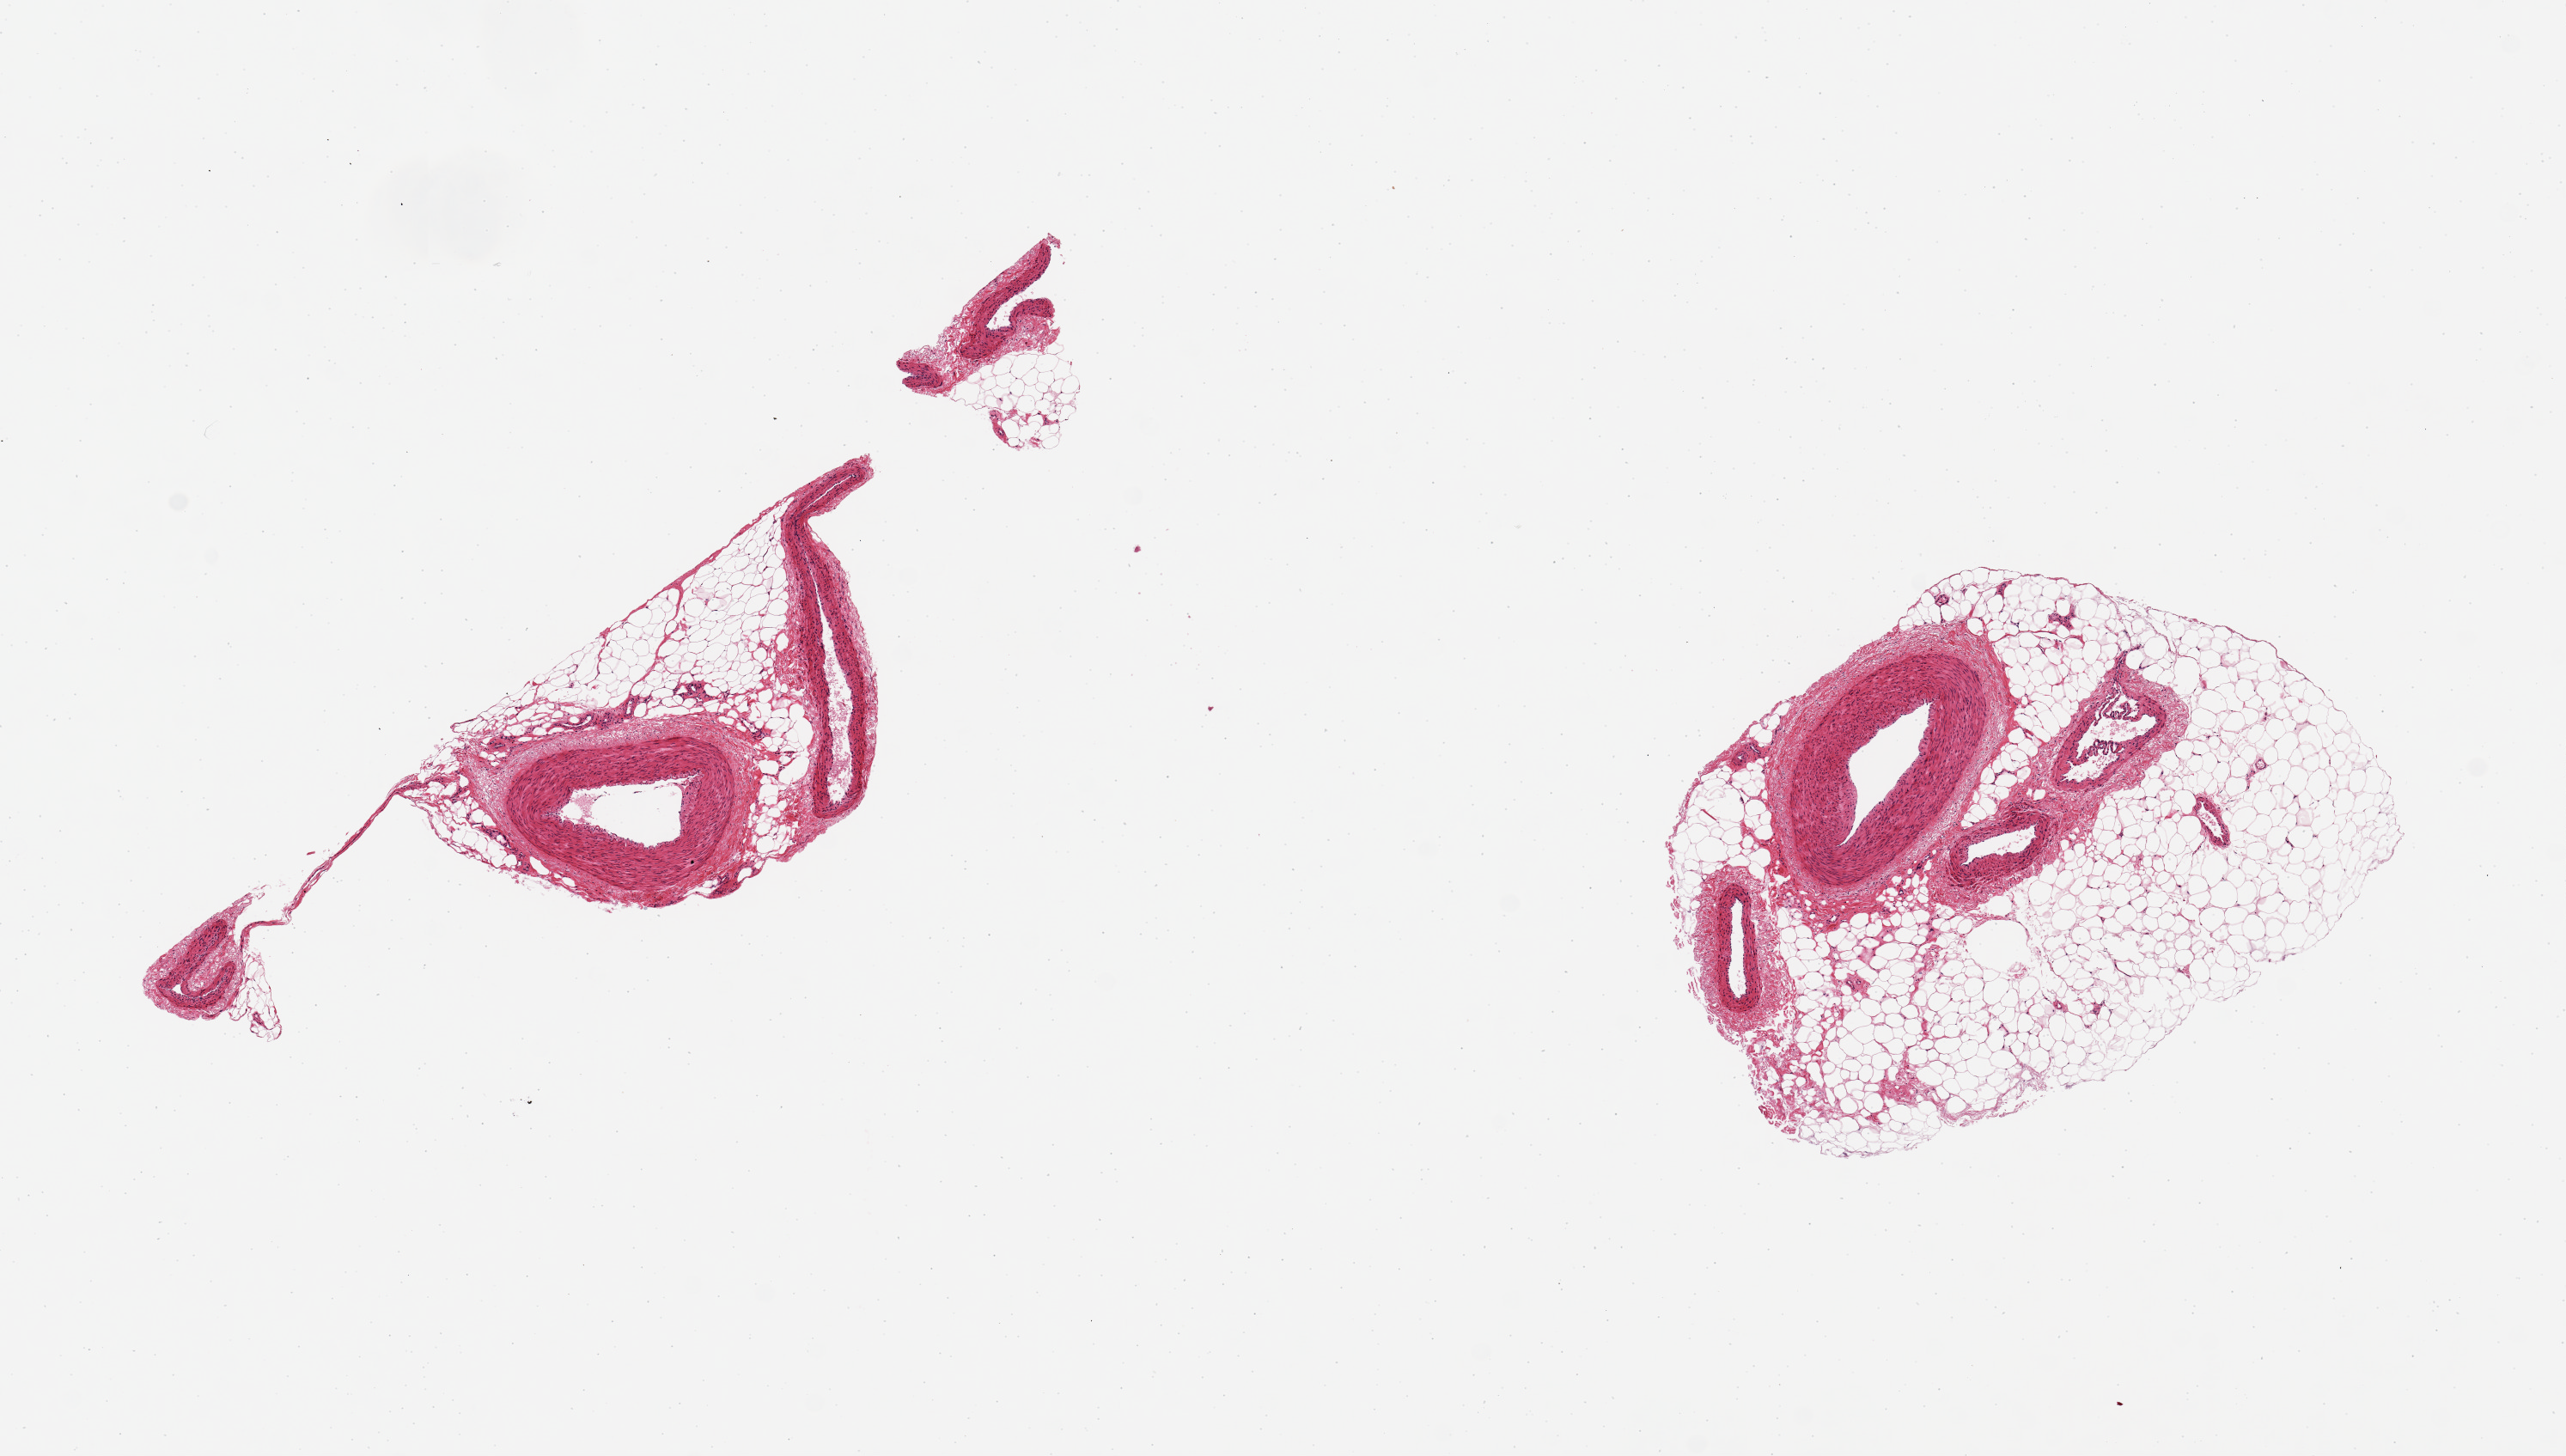
Digitized haematoxylin and eosin-stained section — low-resolution overview of the scanned area, about 11.8 x 6.7 mm. PAXgene-fixed paraffin-embedded (PFPE) section. Section of tibial artery (target tissue). Donor tissue sample. Male donor.
Review note (as recorded): 2 pieces ~1.5mm. NOTE: up to 1.5mm layer of adherent fat and smaller vessels.